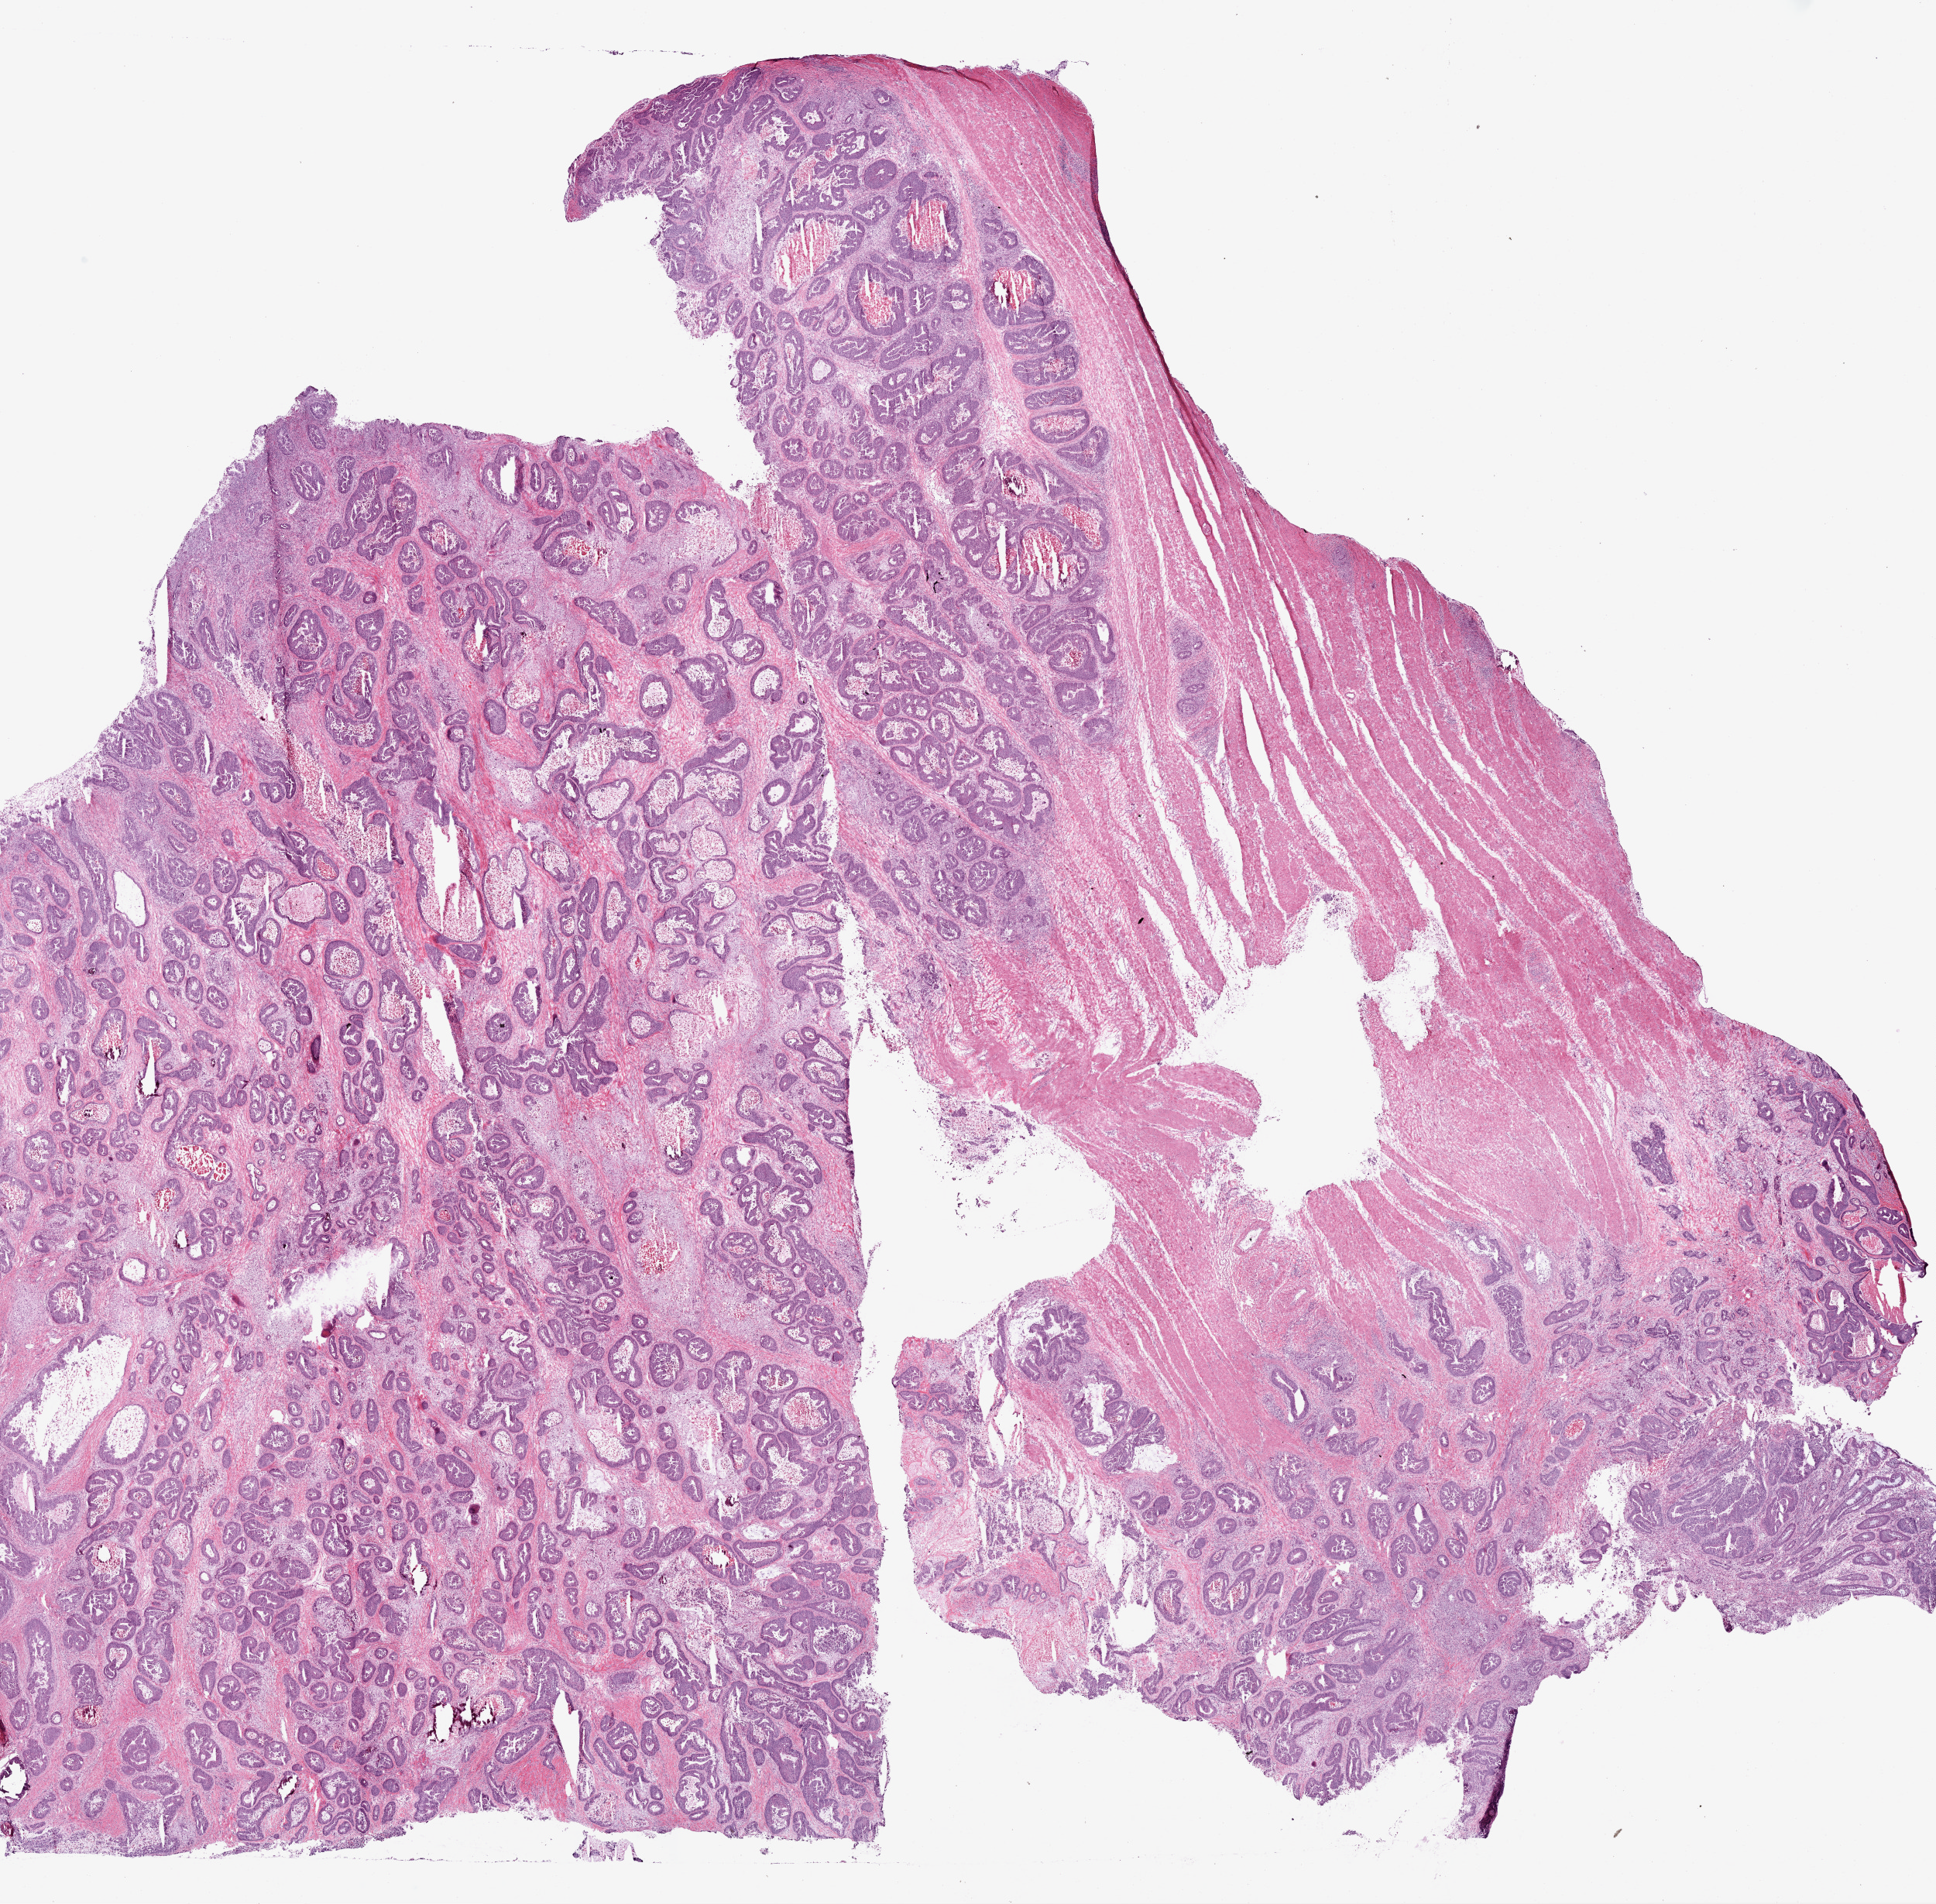
Digitized H&E-stained tissue section (whole slide) — a low-resolution overview of the entire scanned area, about 20.1 x 19.7 mm (slide scanned at 20x); frozen section; colon, primary tumour sample. Female, age 82 years at initial diagnosis. Pathologist review of this section (percent, as recorded): tumour cells 77%, tumour nuclei 75%, normal cells 0%, stromal cells 20%, necrosis 3%. Inflammatory infiltration, as recorded: lymphocyte infiltration 5%, monocyte infiltration 1%, neutrophil infiltration 5%.
AJCC pathologic stage: IIIA. Pathologic diagnosis: Adenocarcinoma, NOS (sigmoid colon). Lymph nodes positive (case pathology): 1 of 18 examined.